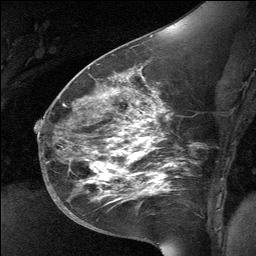
Breast MRI (dynamic contrast-enhanced), one sagittal slice. Slice 37 of 64 in the series (ordered by position). Dynamic contrast-enhanced study with each time point stored as its own series, time point 2 of 3 at this slice position (early post-contrast, ordered by acquisition time). 1.5 T. TE 4.8 ms, TR 27 ms. 2 mm slice thickness. 256 × 256 image matrix, field of view 200 × 200 mm. Patient: female, 39 years. From the clinical record (not read from this slice): setting: breast cancer imaged before/during neoadjuvant chemotherapy; receptor status: HER2-positive.
Annotated regions visible in this slice (semi-automatic segmentation, software-assisted and operator-edited):
- analysis volume of interest (the breast-tissue region the enhancement analysis was run in; not a lesion): bounding box [x1, y1, x2, y2] px = [70, 69, 174, 224]
- tumour enhancement mask (voxels above the 90 % enhancement threshold inside the analysis volume of interest): [88, 138, 163, 193]